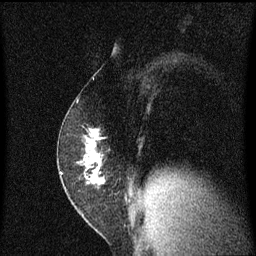
Breast MRI (dynamic contrast-enhanced), one sagittal slice; dynamic contrast-enhanced series, image 2 of 3 at this slice position (ordered by acquisition); 1.5 T; TE 4.2 ms, TR 8.4 ms; 2 mm slice thickness; 256 × 256 image matrix, field of view 200 × 200 mm. Patient: female, 52 years. Case-level facts recorded for this patient, not image findings: setting: breast cancer imaged before/during neoadjuvant chemotherapy; receptor status: HER2-positive.
Structures marked on this image (semi-automatically segmented with operator editing):
- analysis volume of interest (the breast-tissue region the enhancement analysis was run in; not a lesion): bounding box [x1, y1, x2, y2] px = [58, 124, 112, 191]
- tumour enhancement mask (voxels above the 70 % enhancement threshold inside the analysis volume of interest): [86, 130, 100, 185]